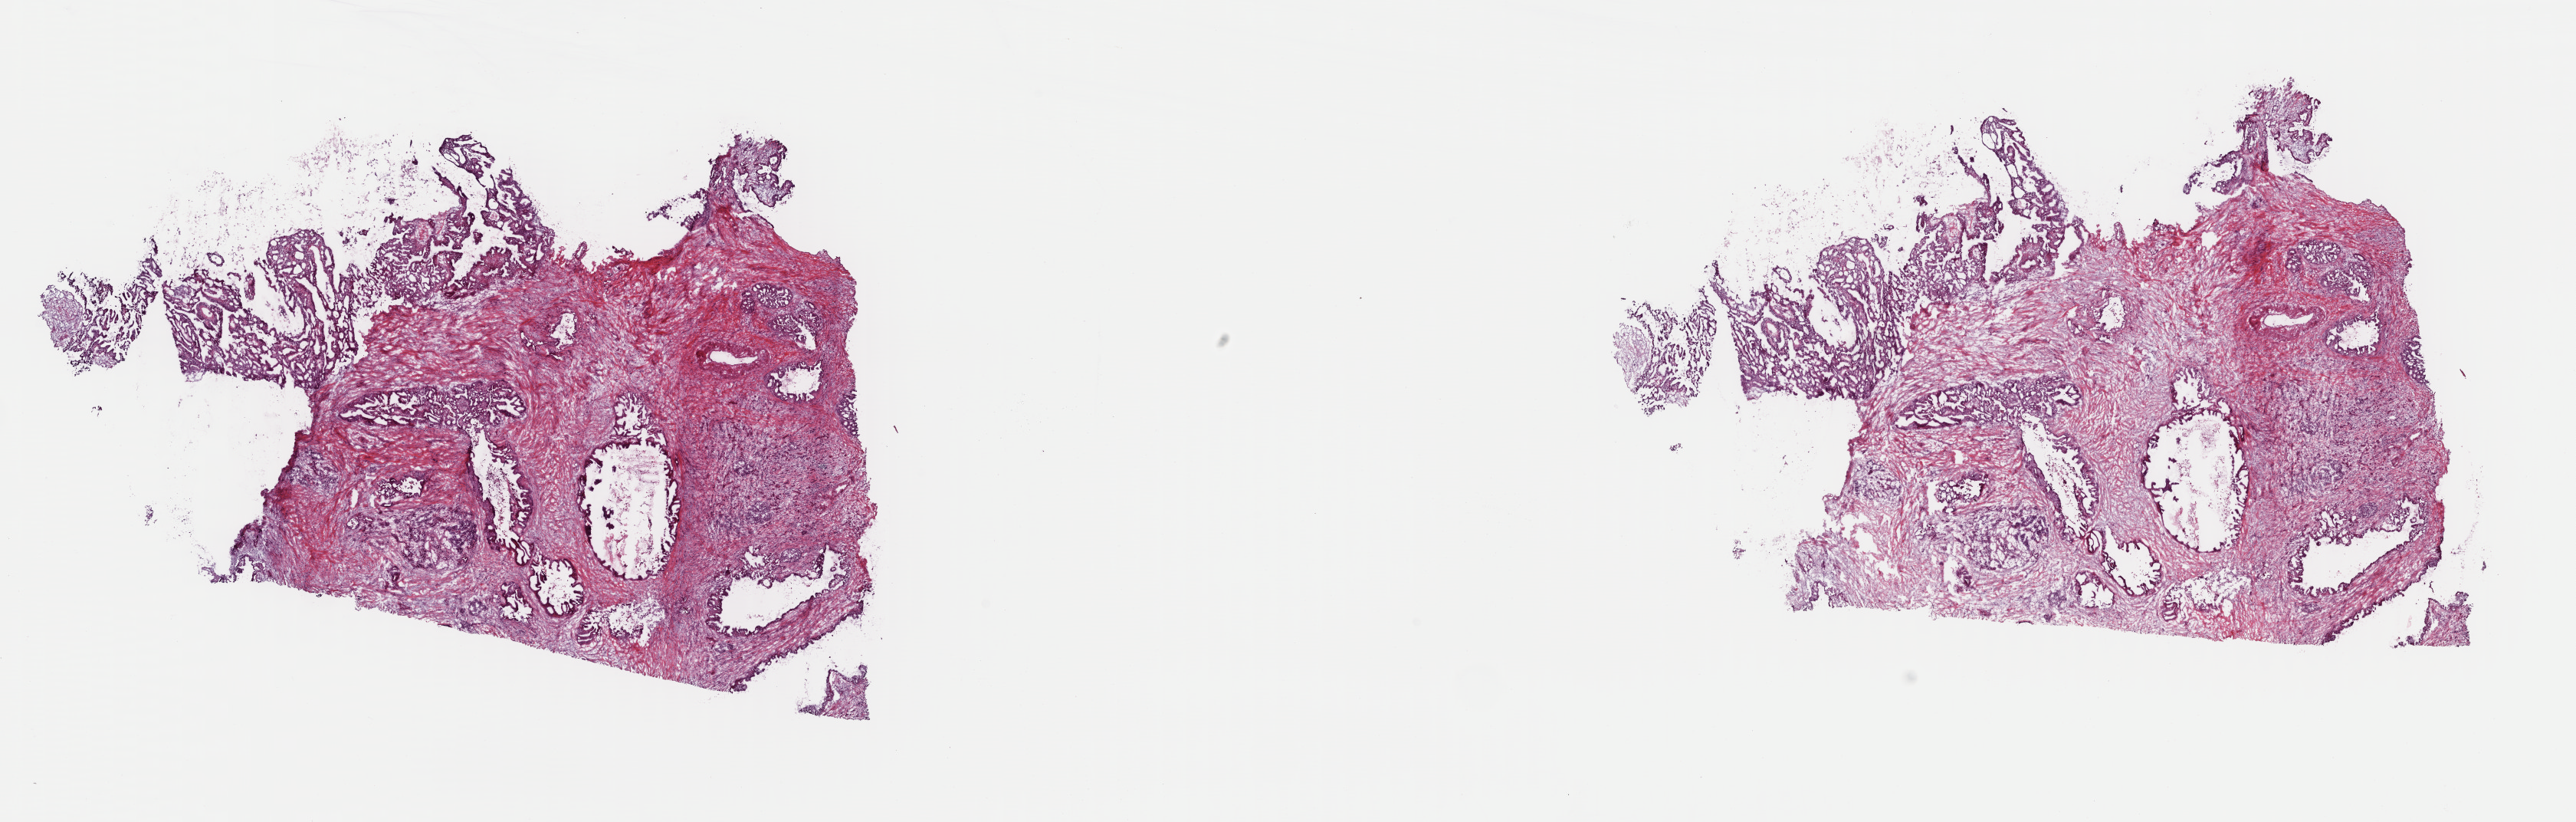
H&E whole-slide image, whole scanned area (about 26.5 x 8.5 mm, from a 40x scan) shown as a low-resolution overview. Frozen section. Primary tumour sample from the pancreas. Male patient; age at initial diagnosis 77 years. Histologic grade: G2 (moderately differentiated). Pathologist review of this section (percent, as recorded): tumour cells 35%, tumour nuclei 75%, normal cells 2%, stromal cells 59%, necrosis 4%. Inflammatory infiltration, as recorded: lymphocyte infiltration 8%, monocyte infiltration 2%, neutrophil infiltration 2%.
Pathologic diagnosis: Infiltrating duct carcinoma, NOS (head of pancreas). Lymph nodes positive (case pathology): 0 of 14 examined. AJCC pathologic stage: IIA (7th edition).